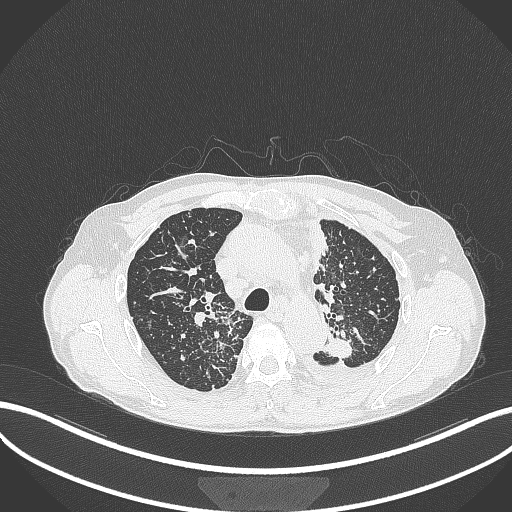
Chest CT, one axial slice. Slice 256 of 325 in the series (ordered by position). Reconstruction kernel B70f. Lung window (W 1500 / L -600 HU). 1 mm slice thickness. 512 × 512 image matrix, field of view 400 × 400 mm. Patient: male, 58 years. Case-level facts recorded for this patient, not image findings: clinical TNM (as recorded): T1c N3 M1.
Outlined on this slice (bounding box drawn by a radiologist):
- lung tumour (recorded histology: adenocarcinoma): bounding box <321,330,357,359> (left, top, right, bottom; pixels)